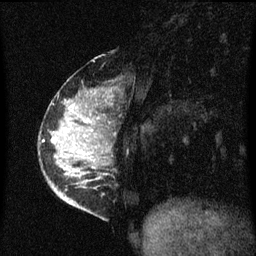
Breast MRI (dynamic contrast-enhanced), one sagittal slice. Slice 19 of 60 in the series (ordered by position). Dynamic contrast-enhanced series, image 2 of 3 at this slice position (ordered by acquisition). 1.5 T. TE 4.2 ms, TR 8.4 ms. 256 × 256 image matrix, field of view 200 × 200 mm. Female patient, age 34 years. Case-level facts recorded for this patient, not image findings: setting: breast cancer imaged before/during neoadjuvant chemotherapy; receptor status: HR-positive, HER2-negative.
Structures marked on this image (semi-automatic segmentation, software-assisted and operator-edited):
- analysis volume of interest (the breast-tissue region the enhancement analysis was run in; not a lesion): bounding box (x1, y1, x2, y2) in pixels: (42, 56, 111, 215)
- tumour enhancement mask (voxels above the 70 % enhancement threshold inside the analysis volume of interest): (72, 104, 75, 145)